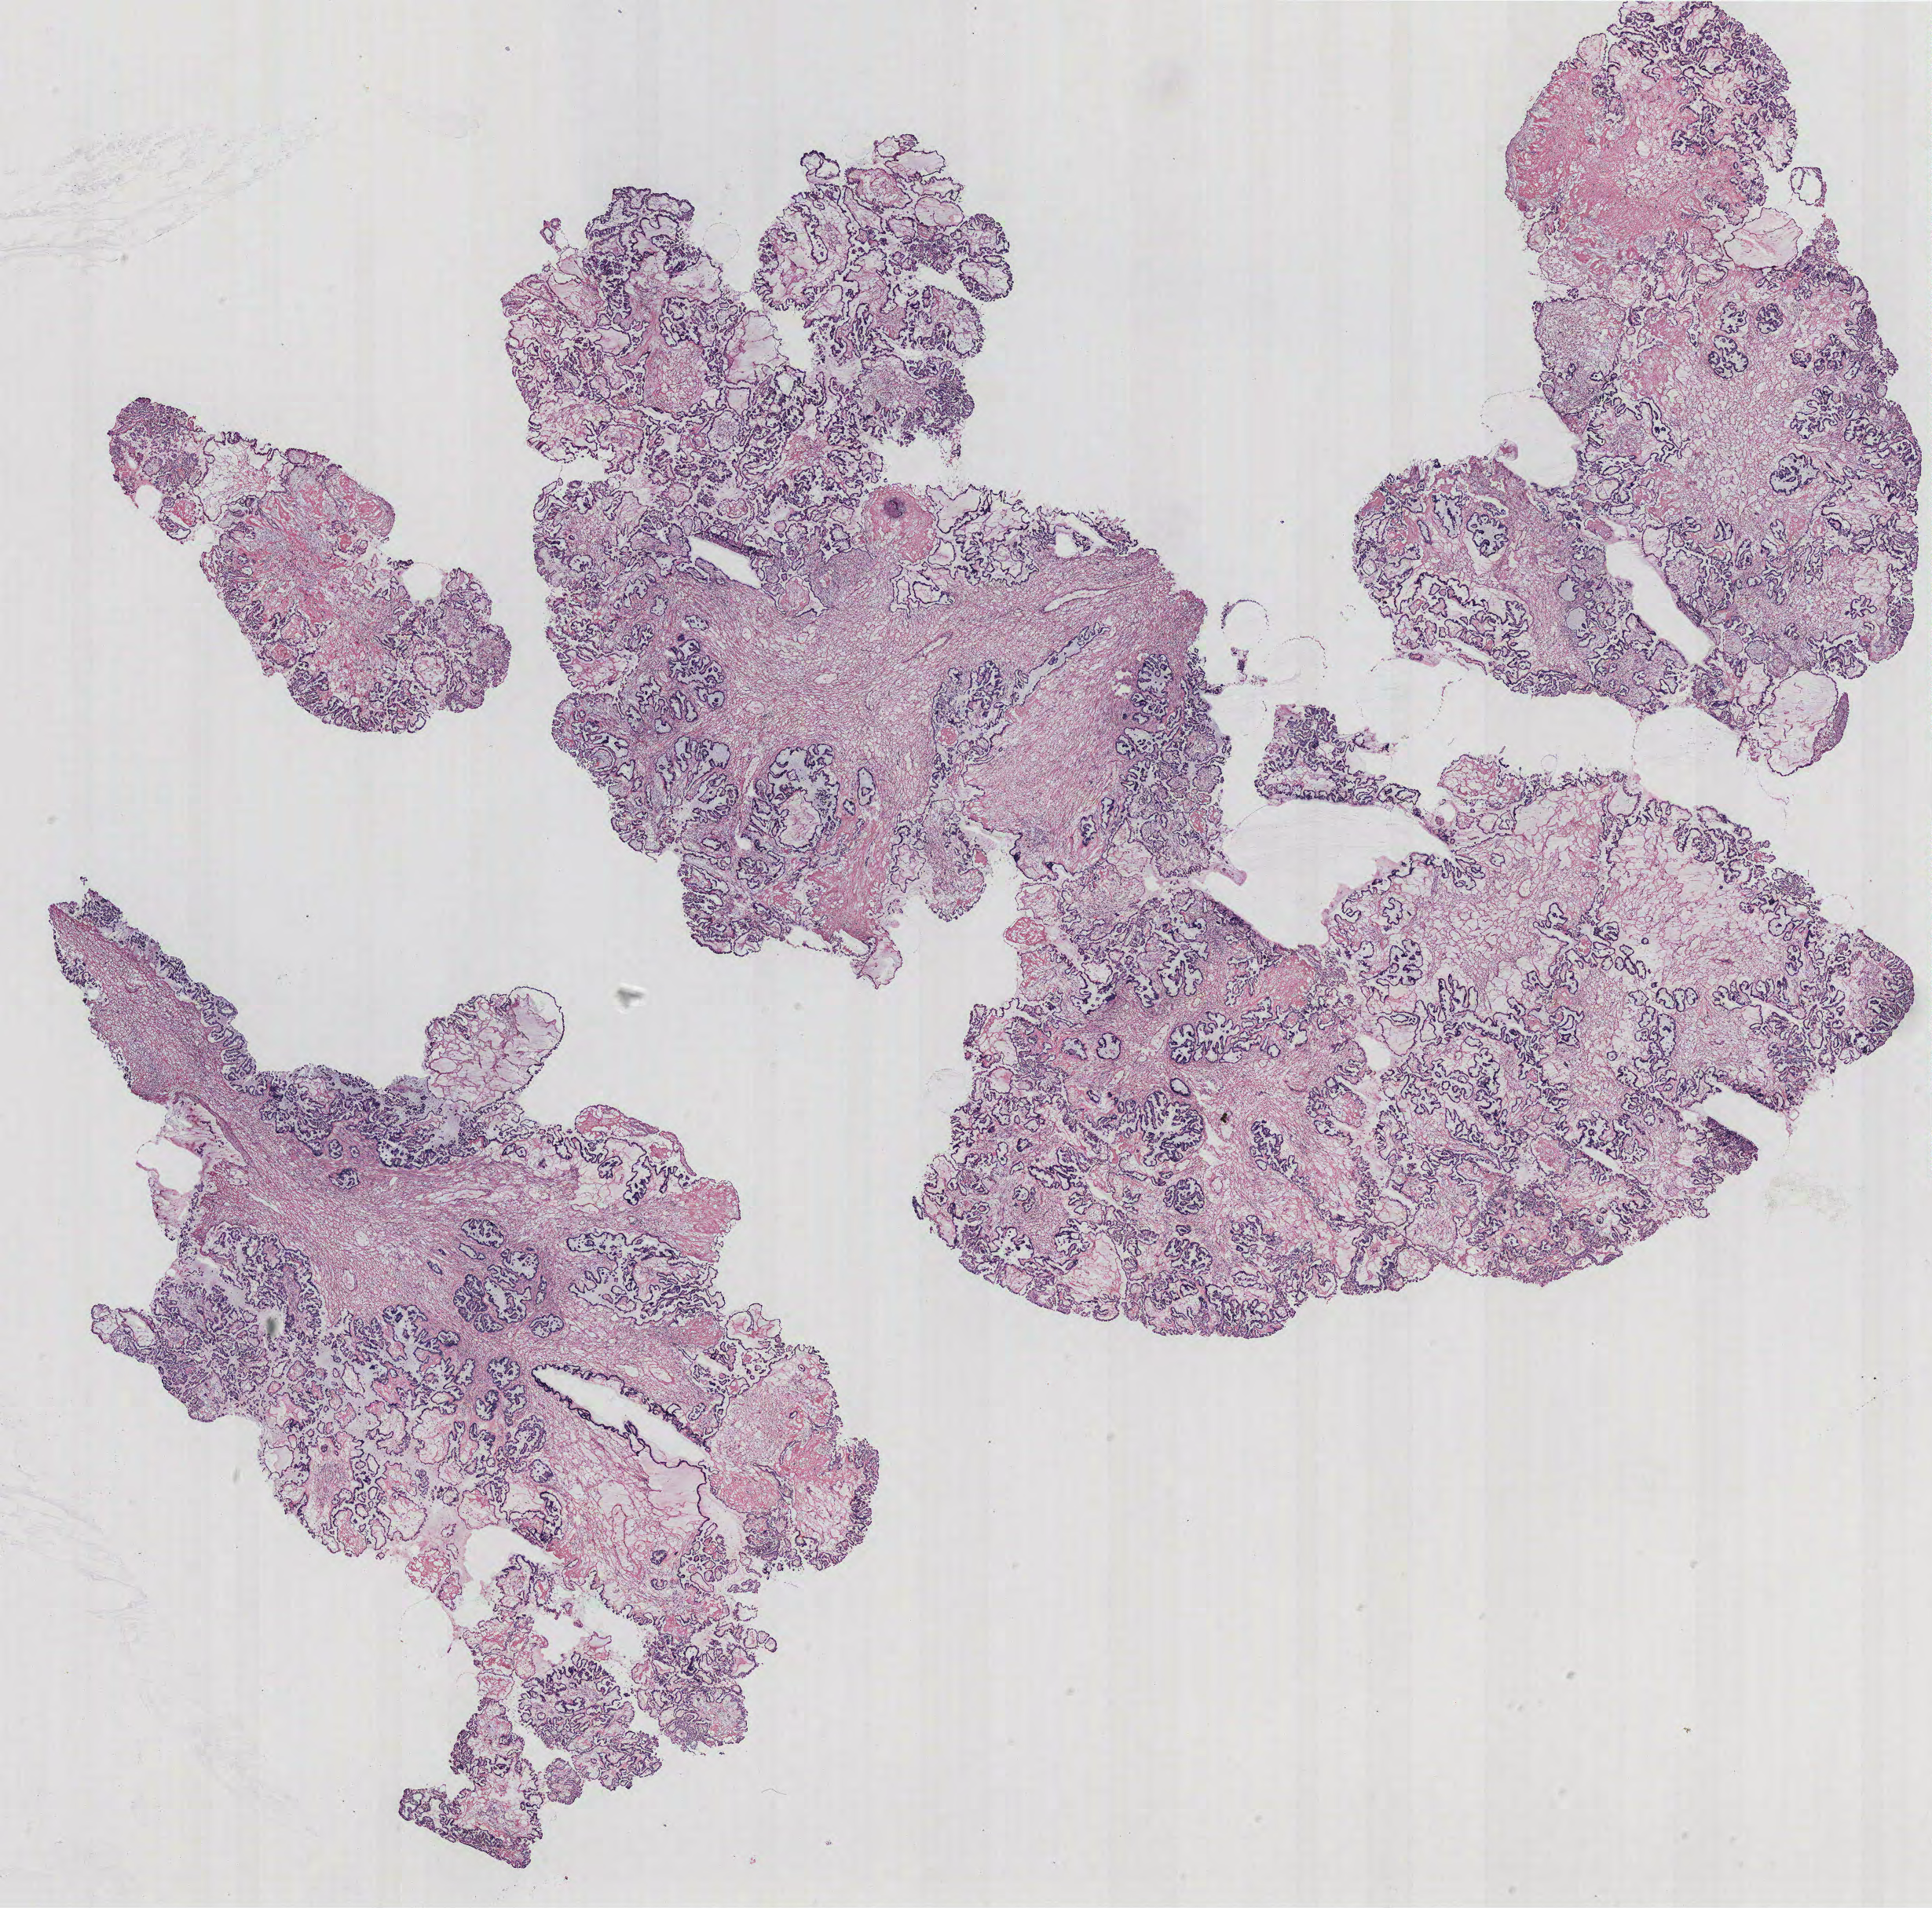
Hematoxylin and eosin (H&E) stained whole-slide image, whole scanned area (about 19.7 x 19.4 mm) shown as a low-resolution overview. Tumour tissue sample, ovary. Female, 49 y/o.
Diagnosis: Serous adenocarcinoma, NOS. Primary tumour site (as recorded): ovary.